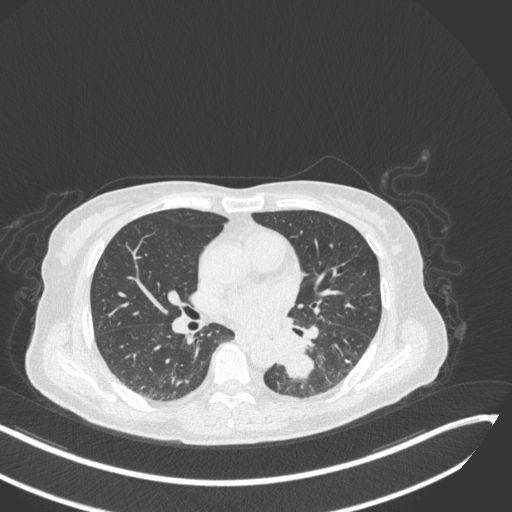
Chest CT, one axial slice; position 135 of 342 along the scan axis; reconstruction kernel B31f; lung window (W 1500 / L -600 HU); 1 mm slice thickness; 512 × 512 image matrix. Patient: female, 64 years. Case-level facts recorded for this patient, not image findings: clinical TNM (as recorded): T3 N1 M1; histopathological grade: G3.
Outlined on this slice (bounding box drawn by a radiologist):
- lung tumour (recorded histology: small cell carcinoma): box from (x=275, y=346) to (x=318, y=383) px